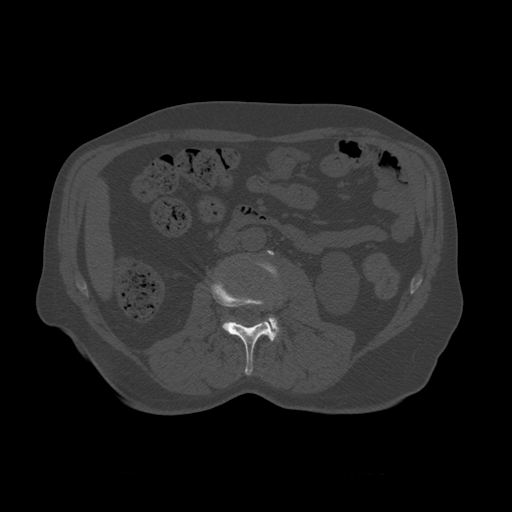
CT including the spine, one axial slice; reconstruction kernel STANDARD; 120 kVp; bone window (W 1800 / L 400 HU); 1.25 mm slice thickness; 512 × 512 image matrix, field of view 405 × 405 mm. Patient age 75 years. Case-level facts recorded for this patient, not image findings: primary cancer: prostate.
Structures marked on this image (semi-automatic segmentation, software-assisted and operator-edited):
- L2 vertebra: bounding box [x1, y1, x2, y2] px = [211, 273, 281, 376]
- L3 vertebra: [231, 250, 281, 342]